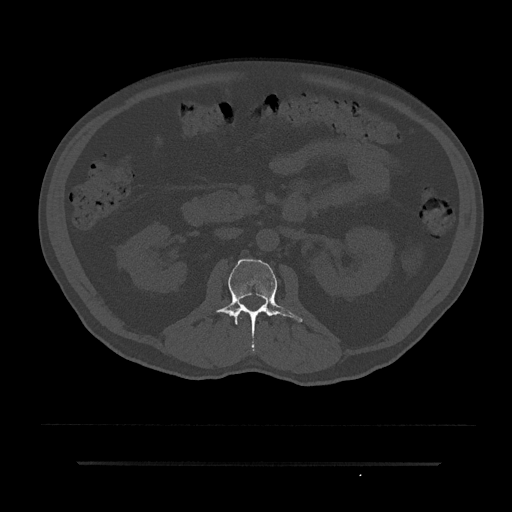
CT including the spine, one axial slice. Slice 79 of 797 in the series (ordered by position). Bone window (W 1800 / L 400 HU). 0.5 mm slice thickness. 512 × 512 image matrix, field of view 464 × 464 mm. Male patient, age 59 years. From the clinical record (not read from this slice): primary cancer: bile ducts.
Structures marked on this image (semi-automatically segmented with operator editing):
- L1 vertebra: bounding box [x1, y1, x2, y2] px = [236, 311, 242, 321]
- L2 vertebra: [208, 259, 303, 348]